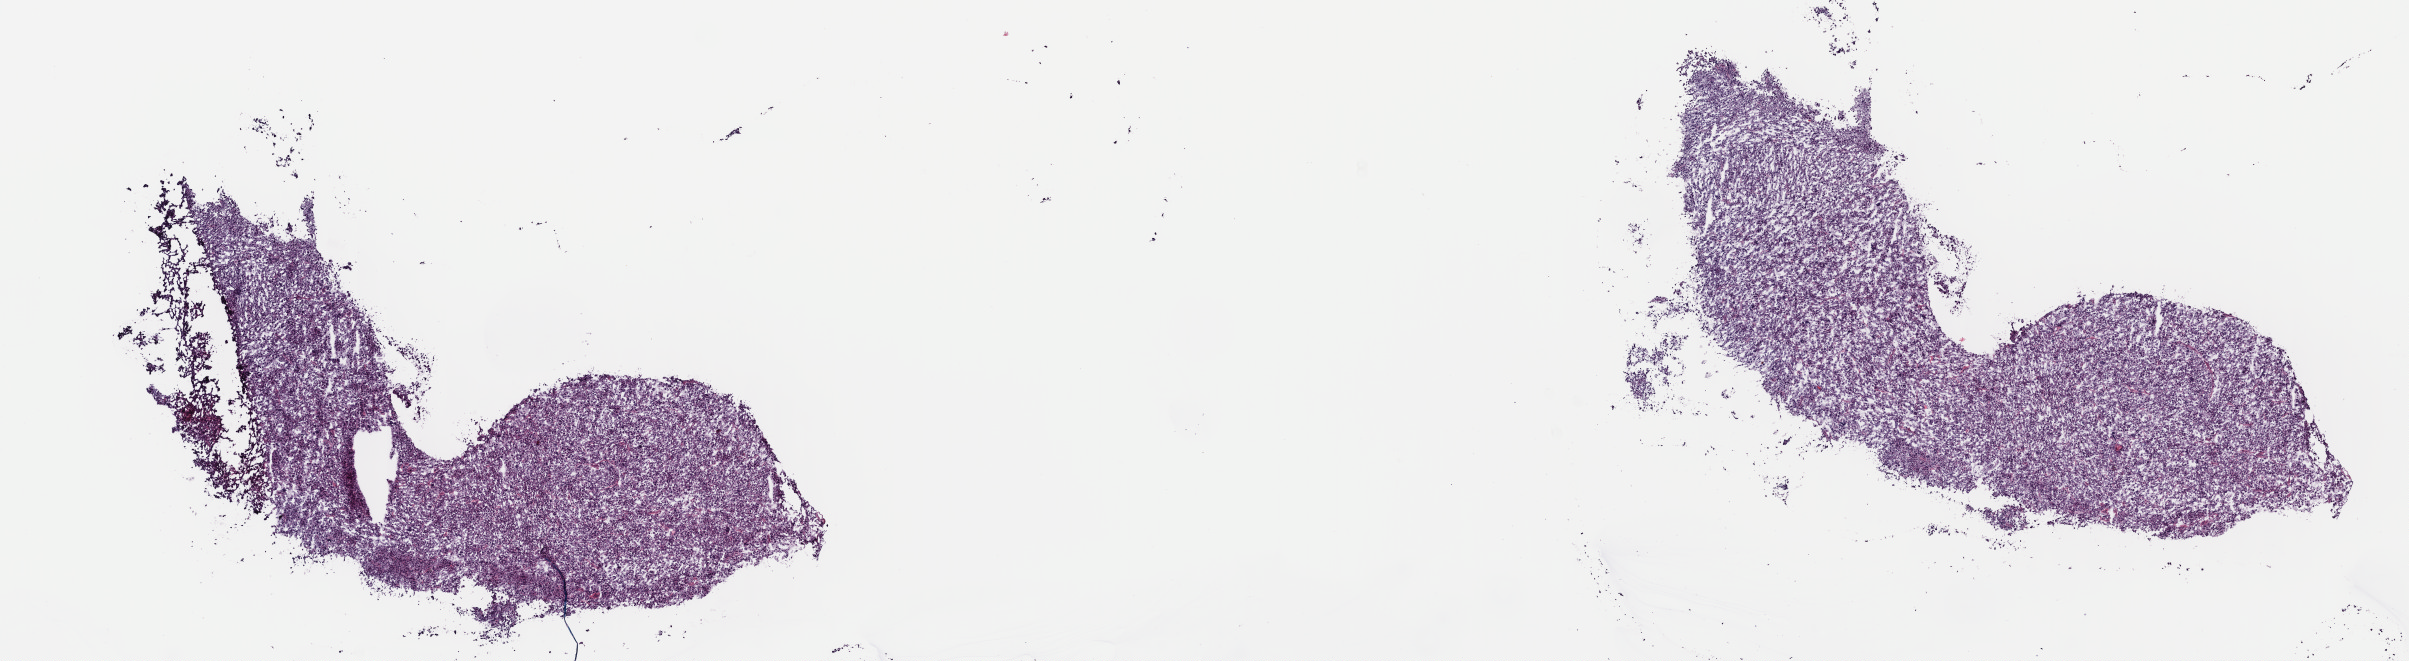
Whole-slide histology image, Hematoxylin and eosin (H&E) stained — low-resolution overview of the scanned area, about 18.9 x 5.2 mm; frozen section from the top of the tissue portion; uterus, primary tumour sample. Patient: female, age at initial diagnosis 60 years. Composition of this section per pathologist review: tumour cells 100%, tumour nuclei 97%.
Pathologic diagnosis: Leiomyosarcoma, NOS.